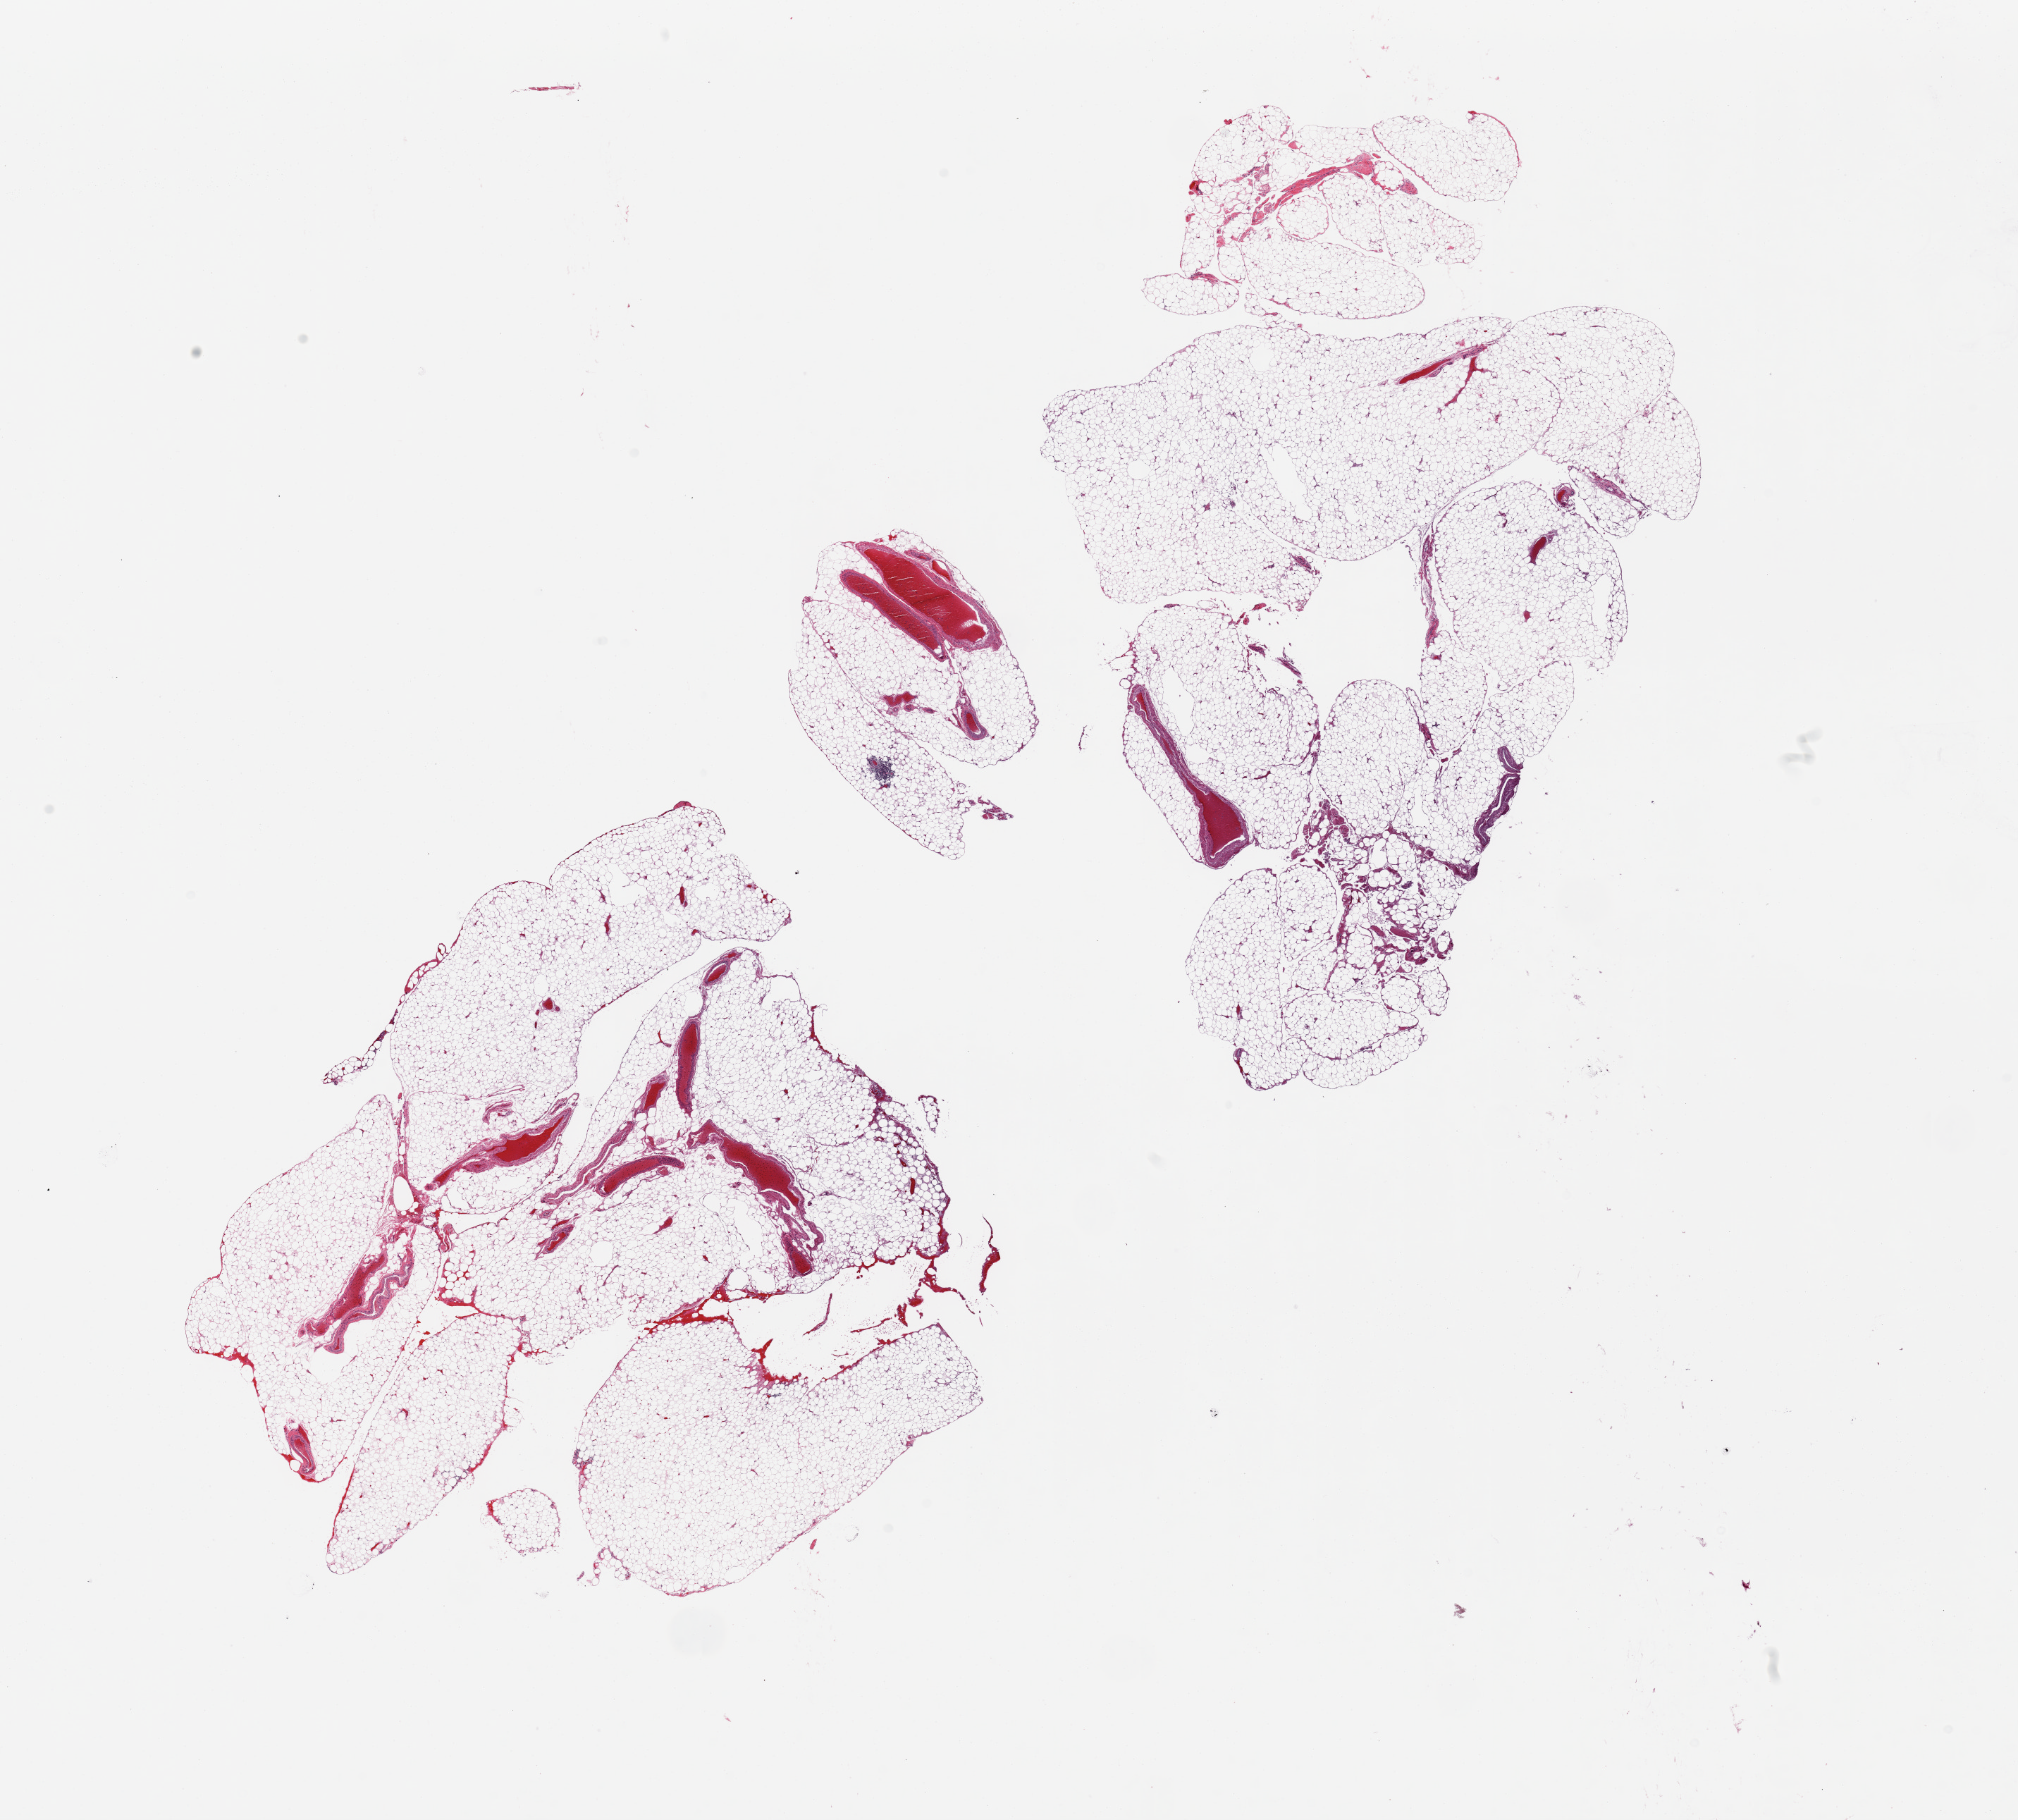
Digitized H&E-stained section, low-resolution overview of the scanned area, about 22.6 x 20.4 mm (acquisition: 20x scan). PAXgene-fixed paraffin-embedded (PFPE) section. Section of omentum (target tissue). Donor tissue sample.
Pathologist's review note for this sample: 2 pieces.